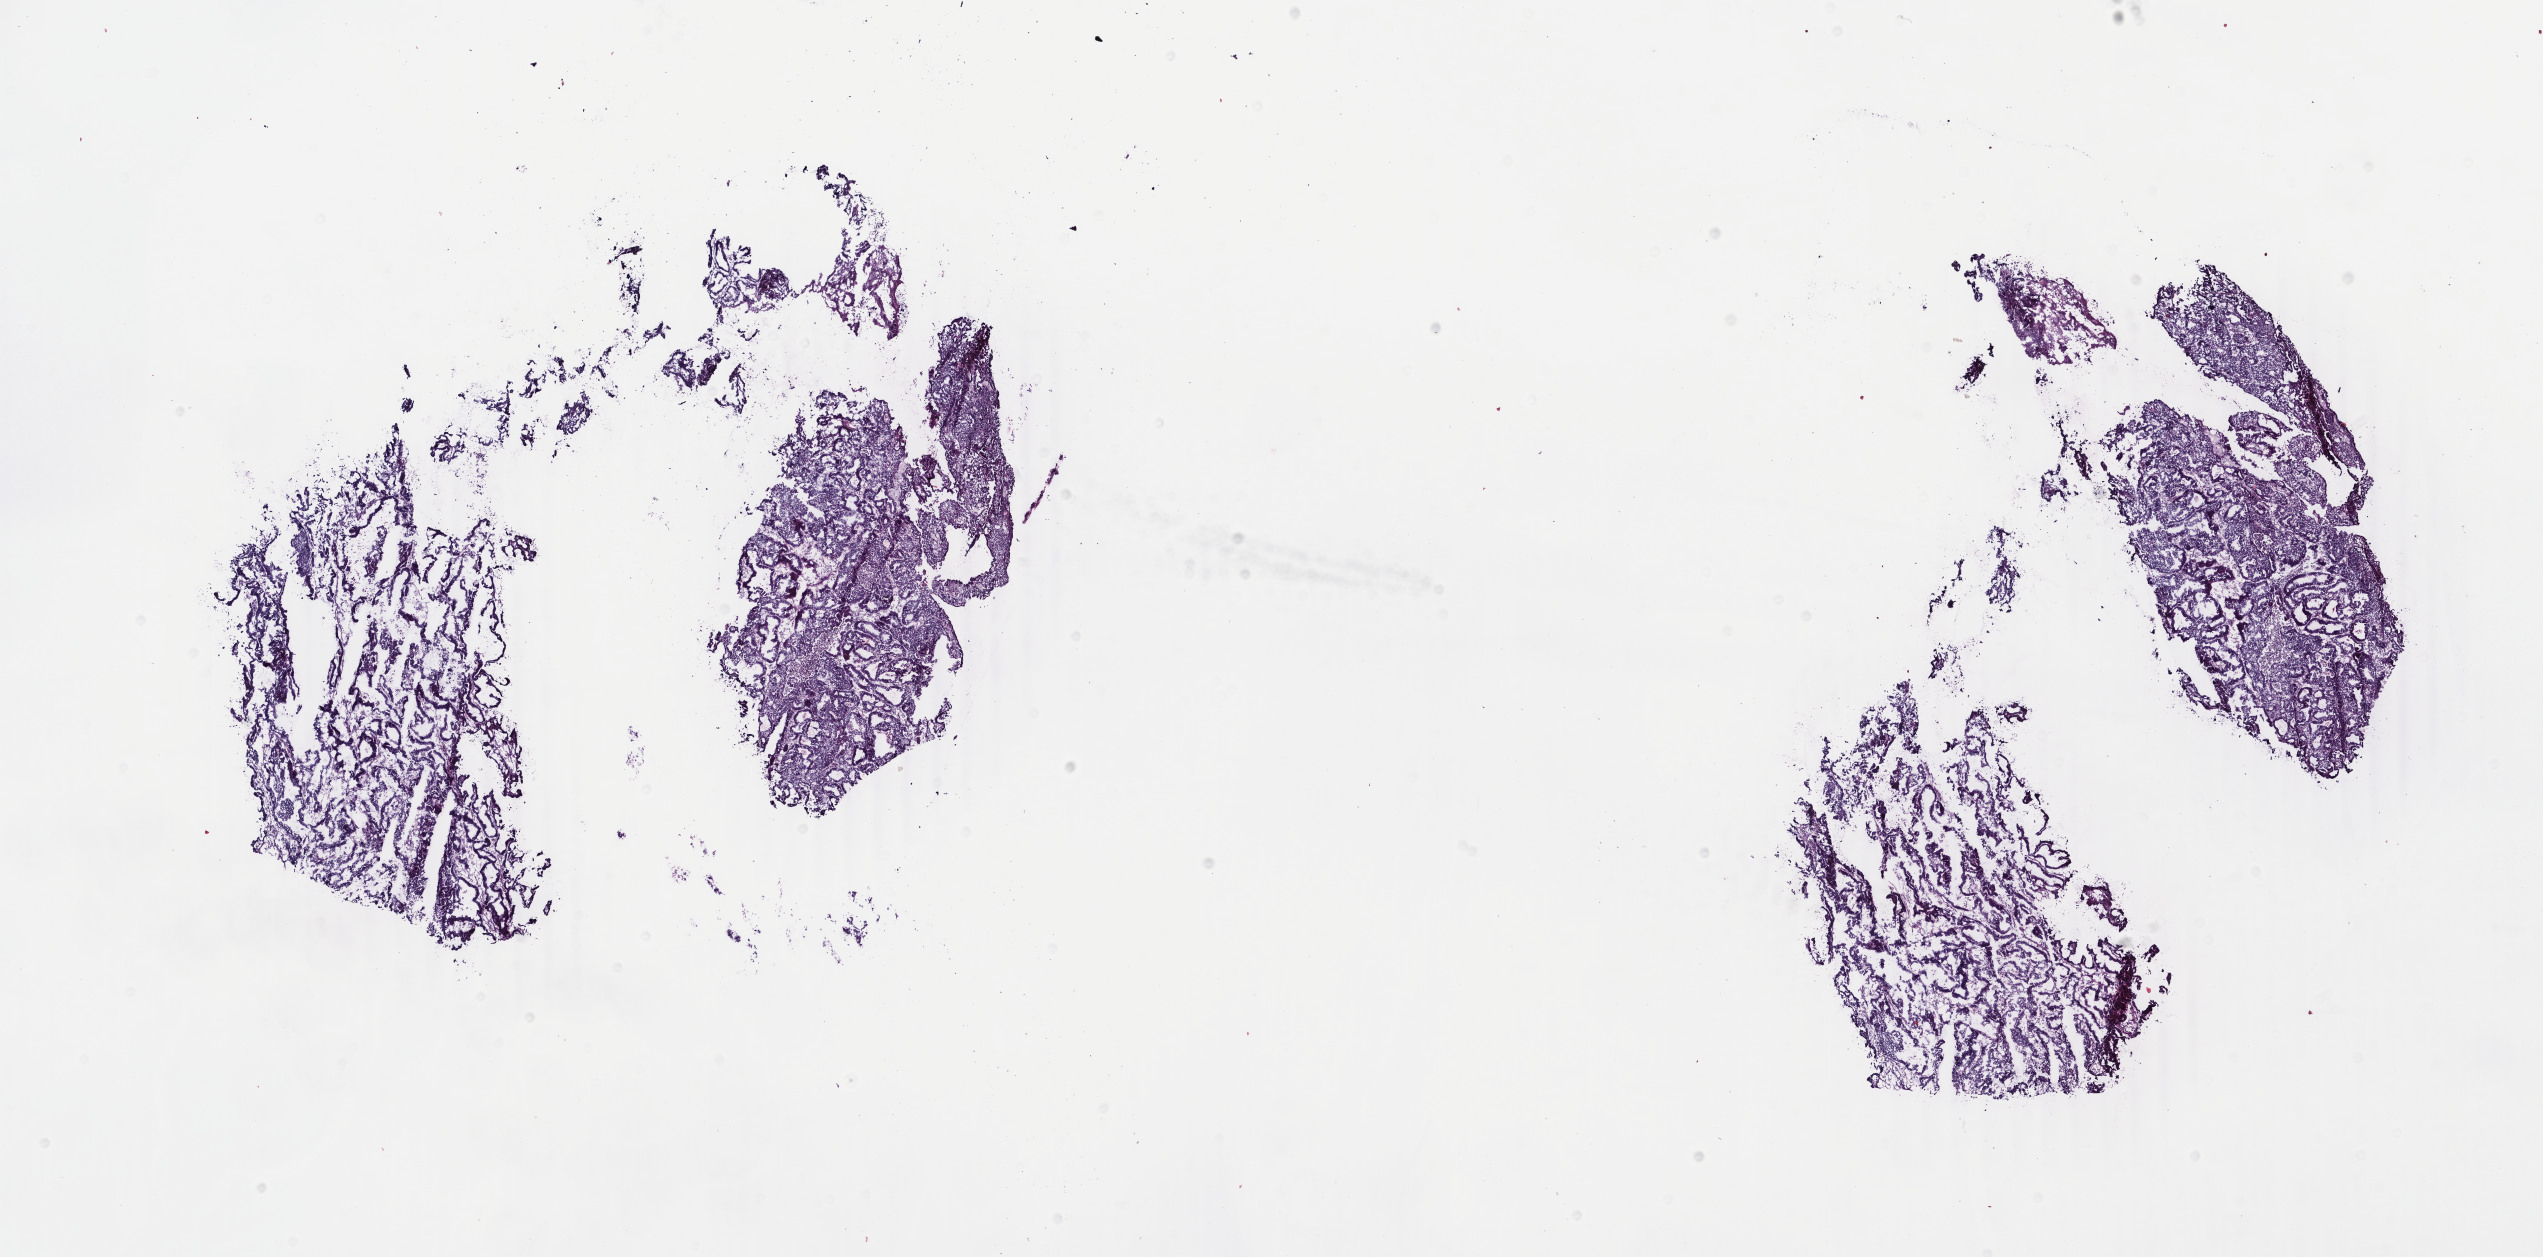
Digitized H&E tissue section (whole slide), whole scanned area (about 20.2 x 10.0 mm, from a 40x scan) shown as a low-resolution overview, frozen section from the top of the tissue portion, uterus, primary tumour sample. Female, age 69 years at initial diagnosis. Histologic grade: G1 (well differentiated). Slide review estimates, as recorded: tumour cells 100%, tumour nuclei 85%, normal cells 0%, stromal cells 0%, necrosis 0%. Inflammatory infiltration, as recorded: lymphocyte infiltration 0%, monocyte infiltration 0%, neutrophil infiltration 0%.
FIGO stage: IA. Diagnosis: Endometrioid adenocarcinoma, NOS (endometrium).